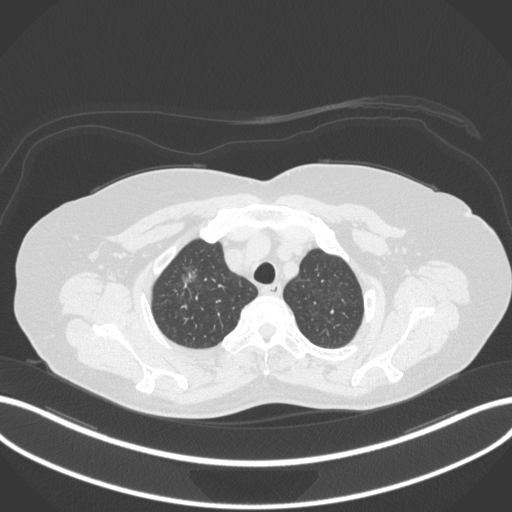
Chest CT, one axial slice; slice 298 of 365 in the series (ordered by position); reconstruction kernel B31f; 120 kVp; lung window (W 1500 / L -600 HU); 1 mm slice thickness; 512 × 512 image matrix. Female patient, age 62 years. From the clinical record (not read from this slice): clinical TNM (as recorded): T1c N0 M0.
Outlined on this slice (rectangle marked by the reading radiologist):
- lung tumour (recorded histology: adenocarcinoma): bounding box <176,254,211,291> (left, top, right, bottom; pixels)